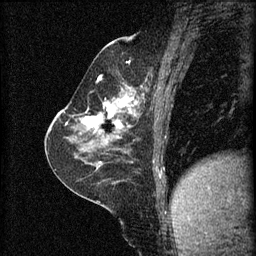
Breast MRI (dynamic contrast-enhanced), one sagittal slice; position 29 of 60 along the scan axis; 3 images stored at this slice position (order not interpretable as contrast timing); 1.5 T; TE 4.2 ms, TR 8.2 ms; 2 mm slice thickness; 256 × 256 image matrix, field of view 180 × 180 mm. Female patient, age 59 years.
Annotated regions visible in this slice (semi-automatically segmented with operator editing):
- analysis volume of interest (the breast-tissue region the enhancement analysis was run in; not a lesion): bounding box (x1, y1, x2, y2) in pixels: (78, 92, 137, 135)
- tumour enhancement mask (voxels above the 70 % enhancement threshold inside the analysis volume of interest): (82, 96, 133, 129)